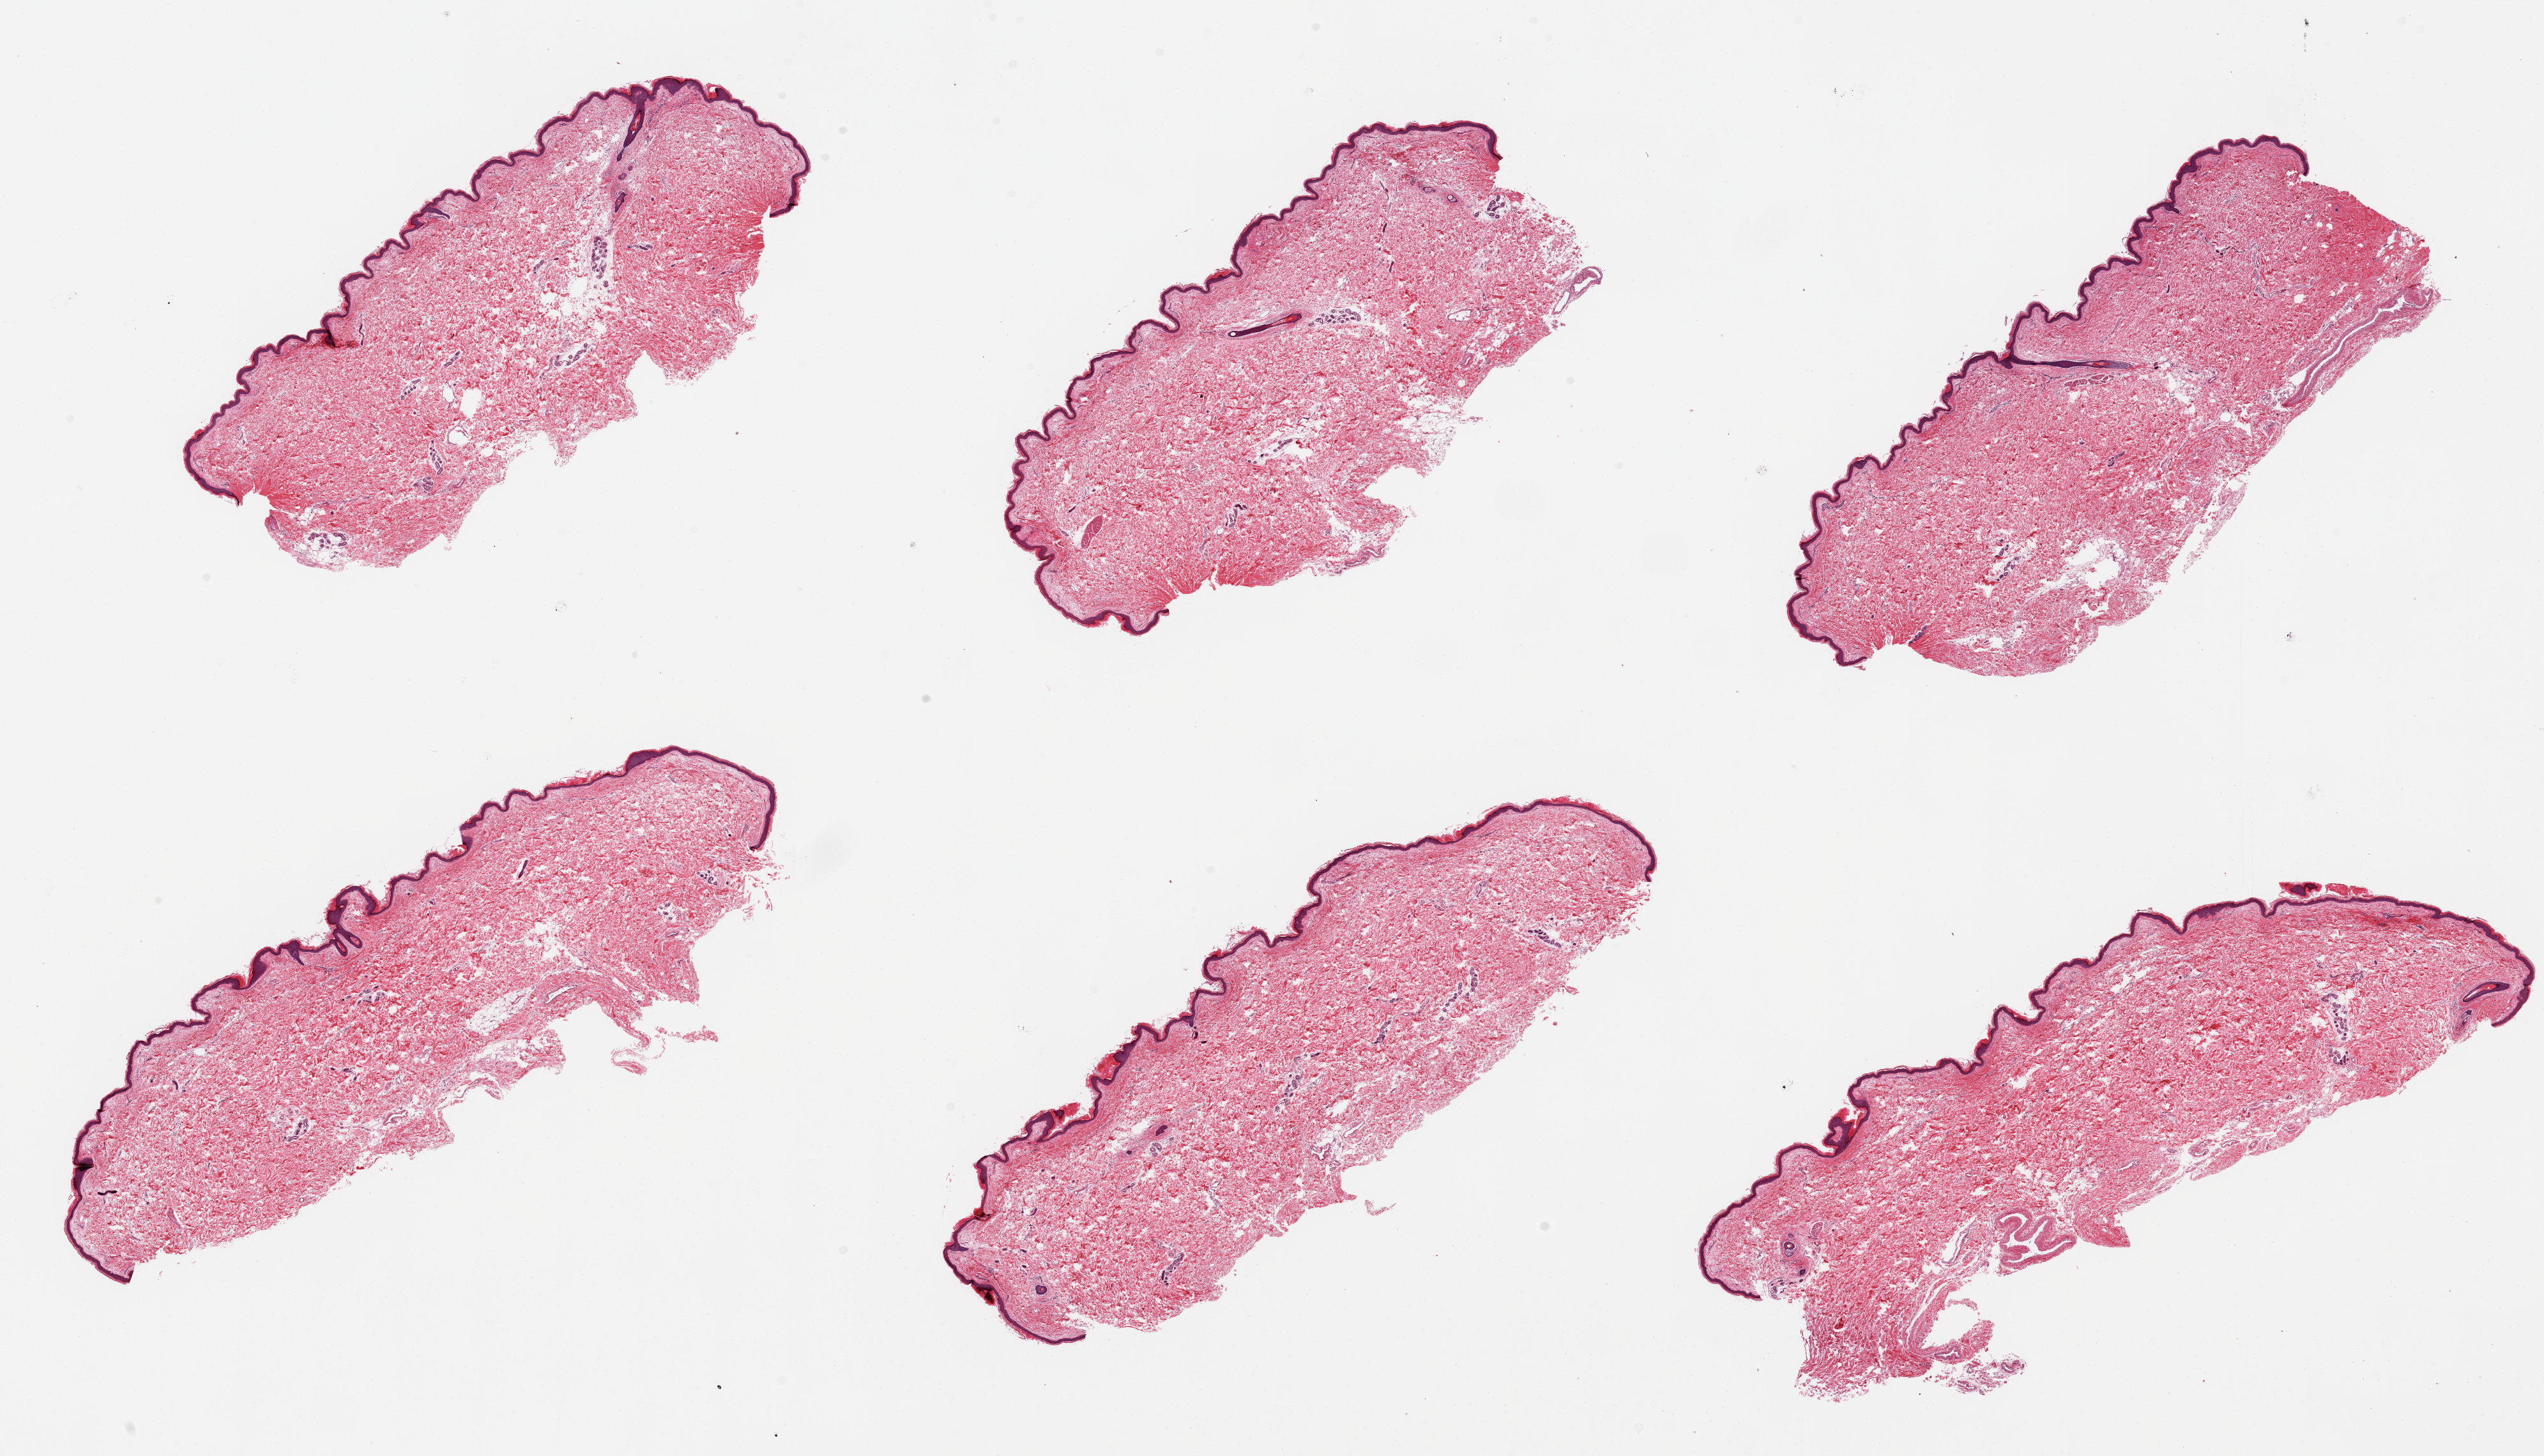
H&E whole-slide image — low-resolution overview of the scanned area, about 31.5 x 18.0 mm. PAXgene-fixed paraffin-embedded (PFPE) section. Sampled site (target tissue): skin of suprapubic region. Donor tissue sample. Donor sex: female.
- pathologist's review note for this sample: 6 pieces; well trimmed